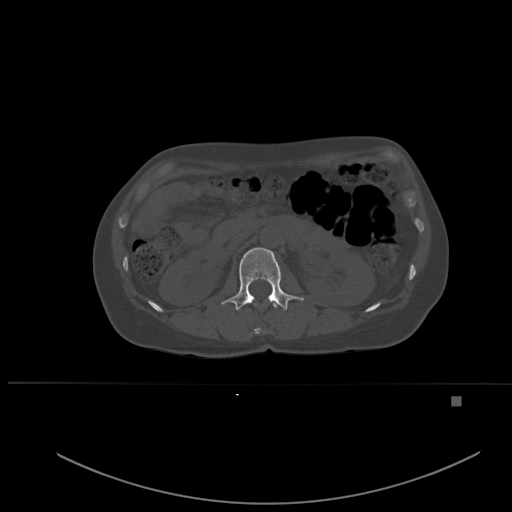
CT including the spine, one axial slice; position 237 of 651 along the scan axis; bone window (W 1800 / L 400 HU); 1.5 mm slice thickness; 512 × 512 image matrix, field of view 443 × 443 mm. Female patient, age 49 years. Case-level facts recorded for this patient, not image findings: primary cancer: breast.
Annotated regions visible in this slice (semi-automatically segmented with operator editing):
- L1 vertebra: bounding box (x1, y1, x2, y2) in pixels: (221, 247, 304, 311)
- T12 vertebra: (254, 303, 277, 334)